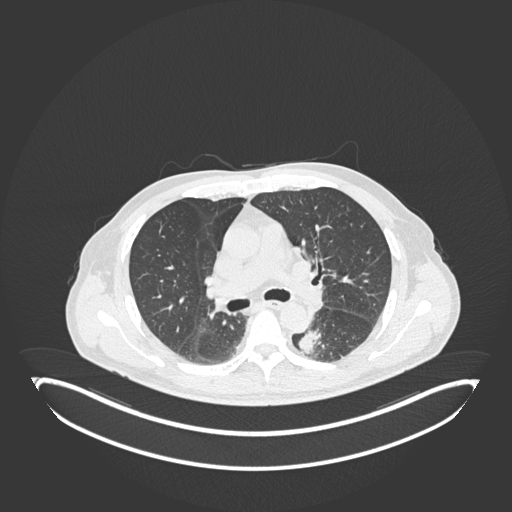
Chest CT, one axial slice; slice 128 of 251 in the series (ordered by position); lung window (W 1500 / L -600 HU); 512 × 512 image matrix, field of view 500 × 500 mm. Patient: male, 72 years. Case-level facts recorded for this patient, not image findings: clinical TNM (as recorded): T2b N0 M1.
Structures marked on this image (bounding box drawn by a radiologist):
- lung tumour (recorded histology: adenocarcinoma): bounding box (x1, y1, x2, y2) in pixels: (293, 327, 330, 363)